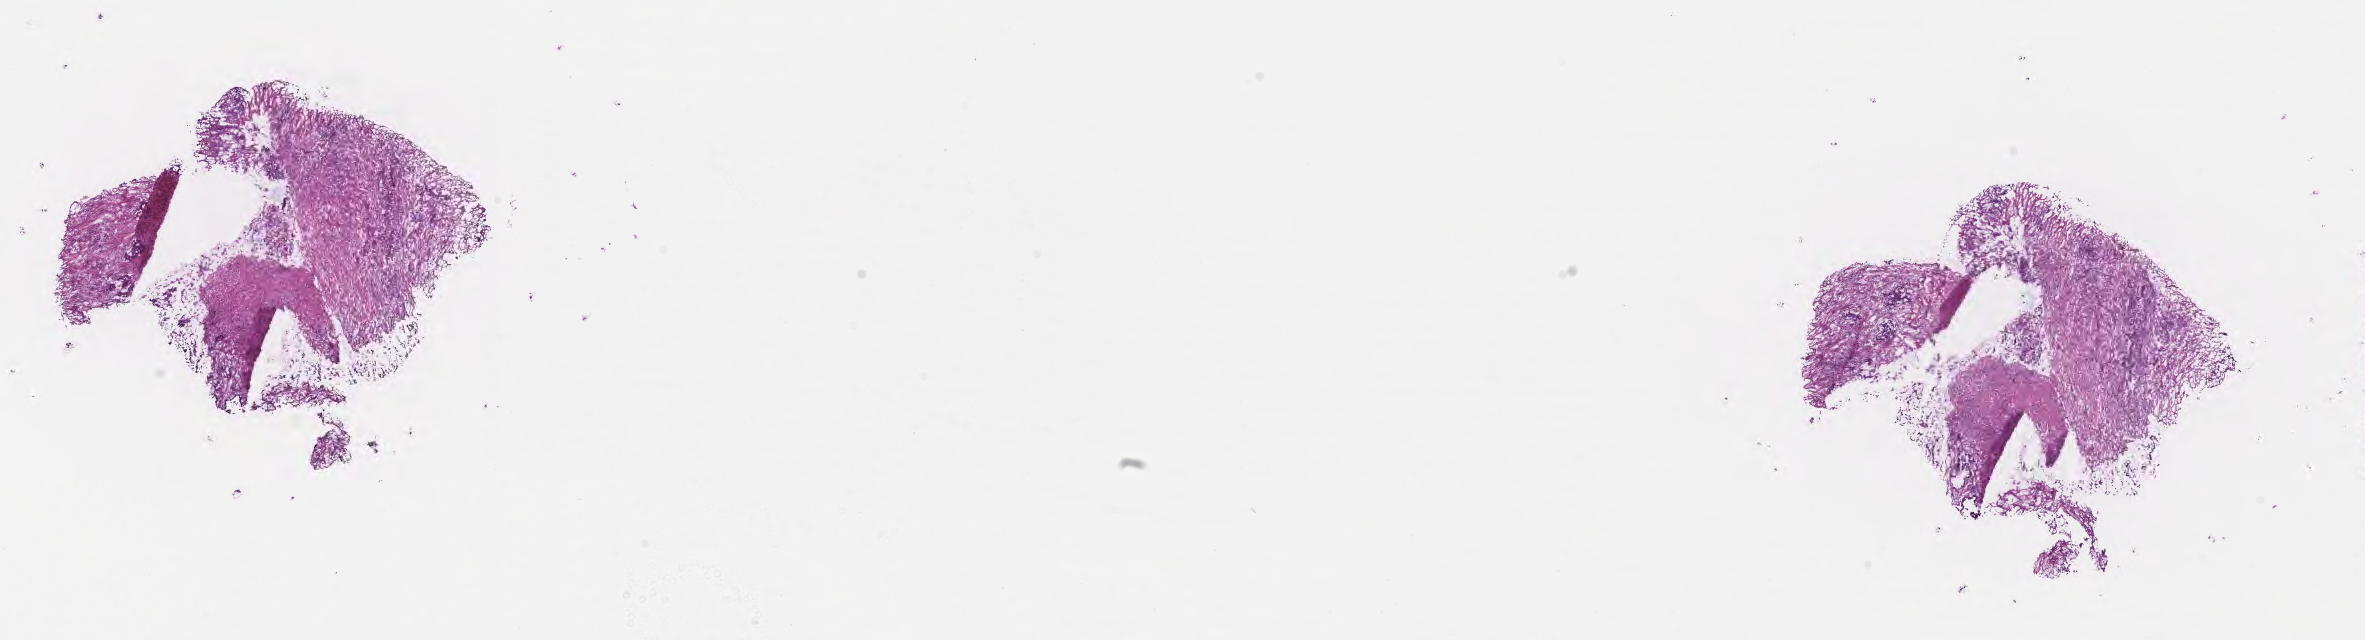
Whole-slide image, H&E stain, whole scanned area (about 19.1 x 5.2 mm) shown as a low-resolution overview. Frozen section (tissue freezing medium). Specimen: primary tumor. Anatomic site: rectosigmoid junction. Patient: female, age at initial diagnosis 68 years.
Diagnosis: Adenocarcinoma, NOS.